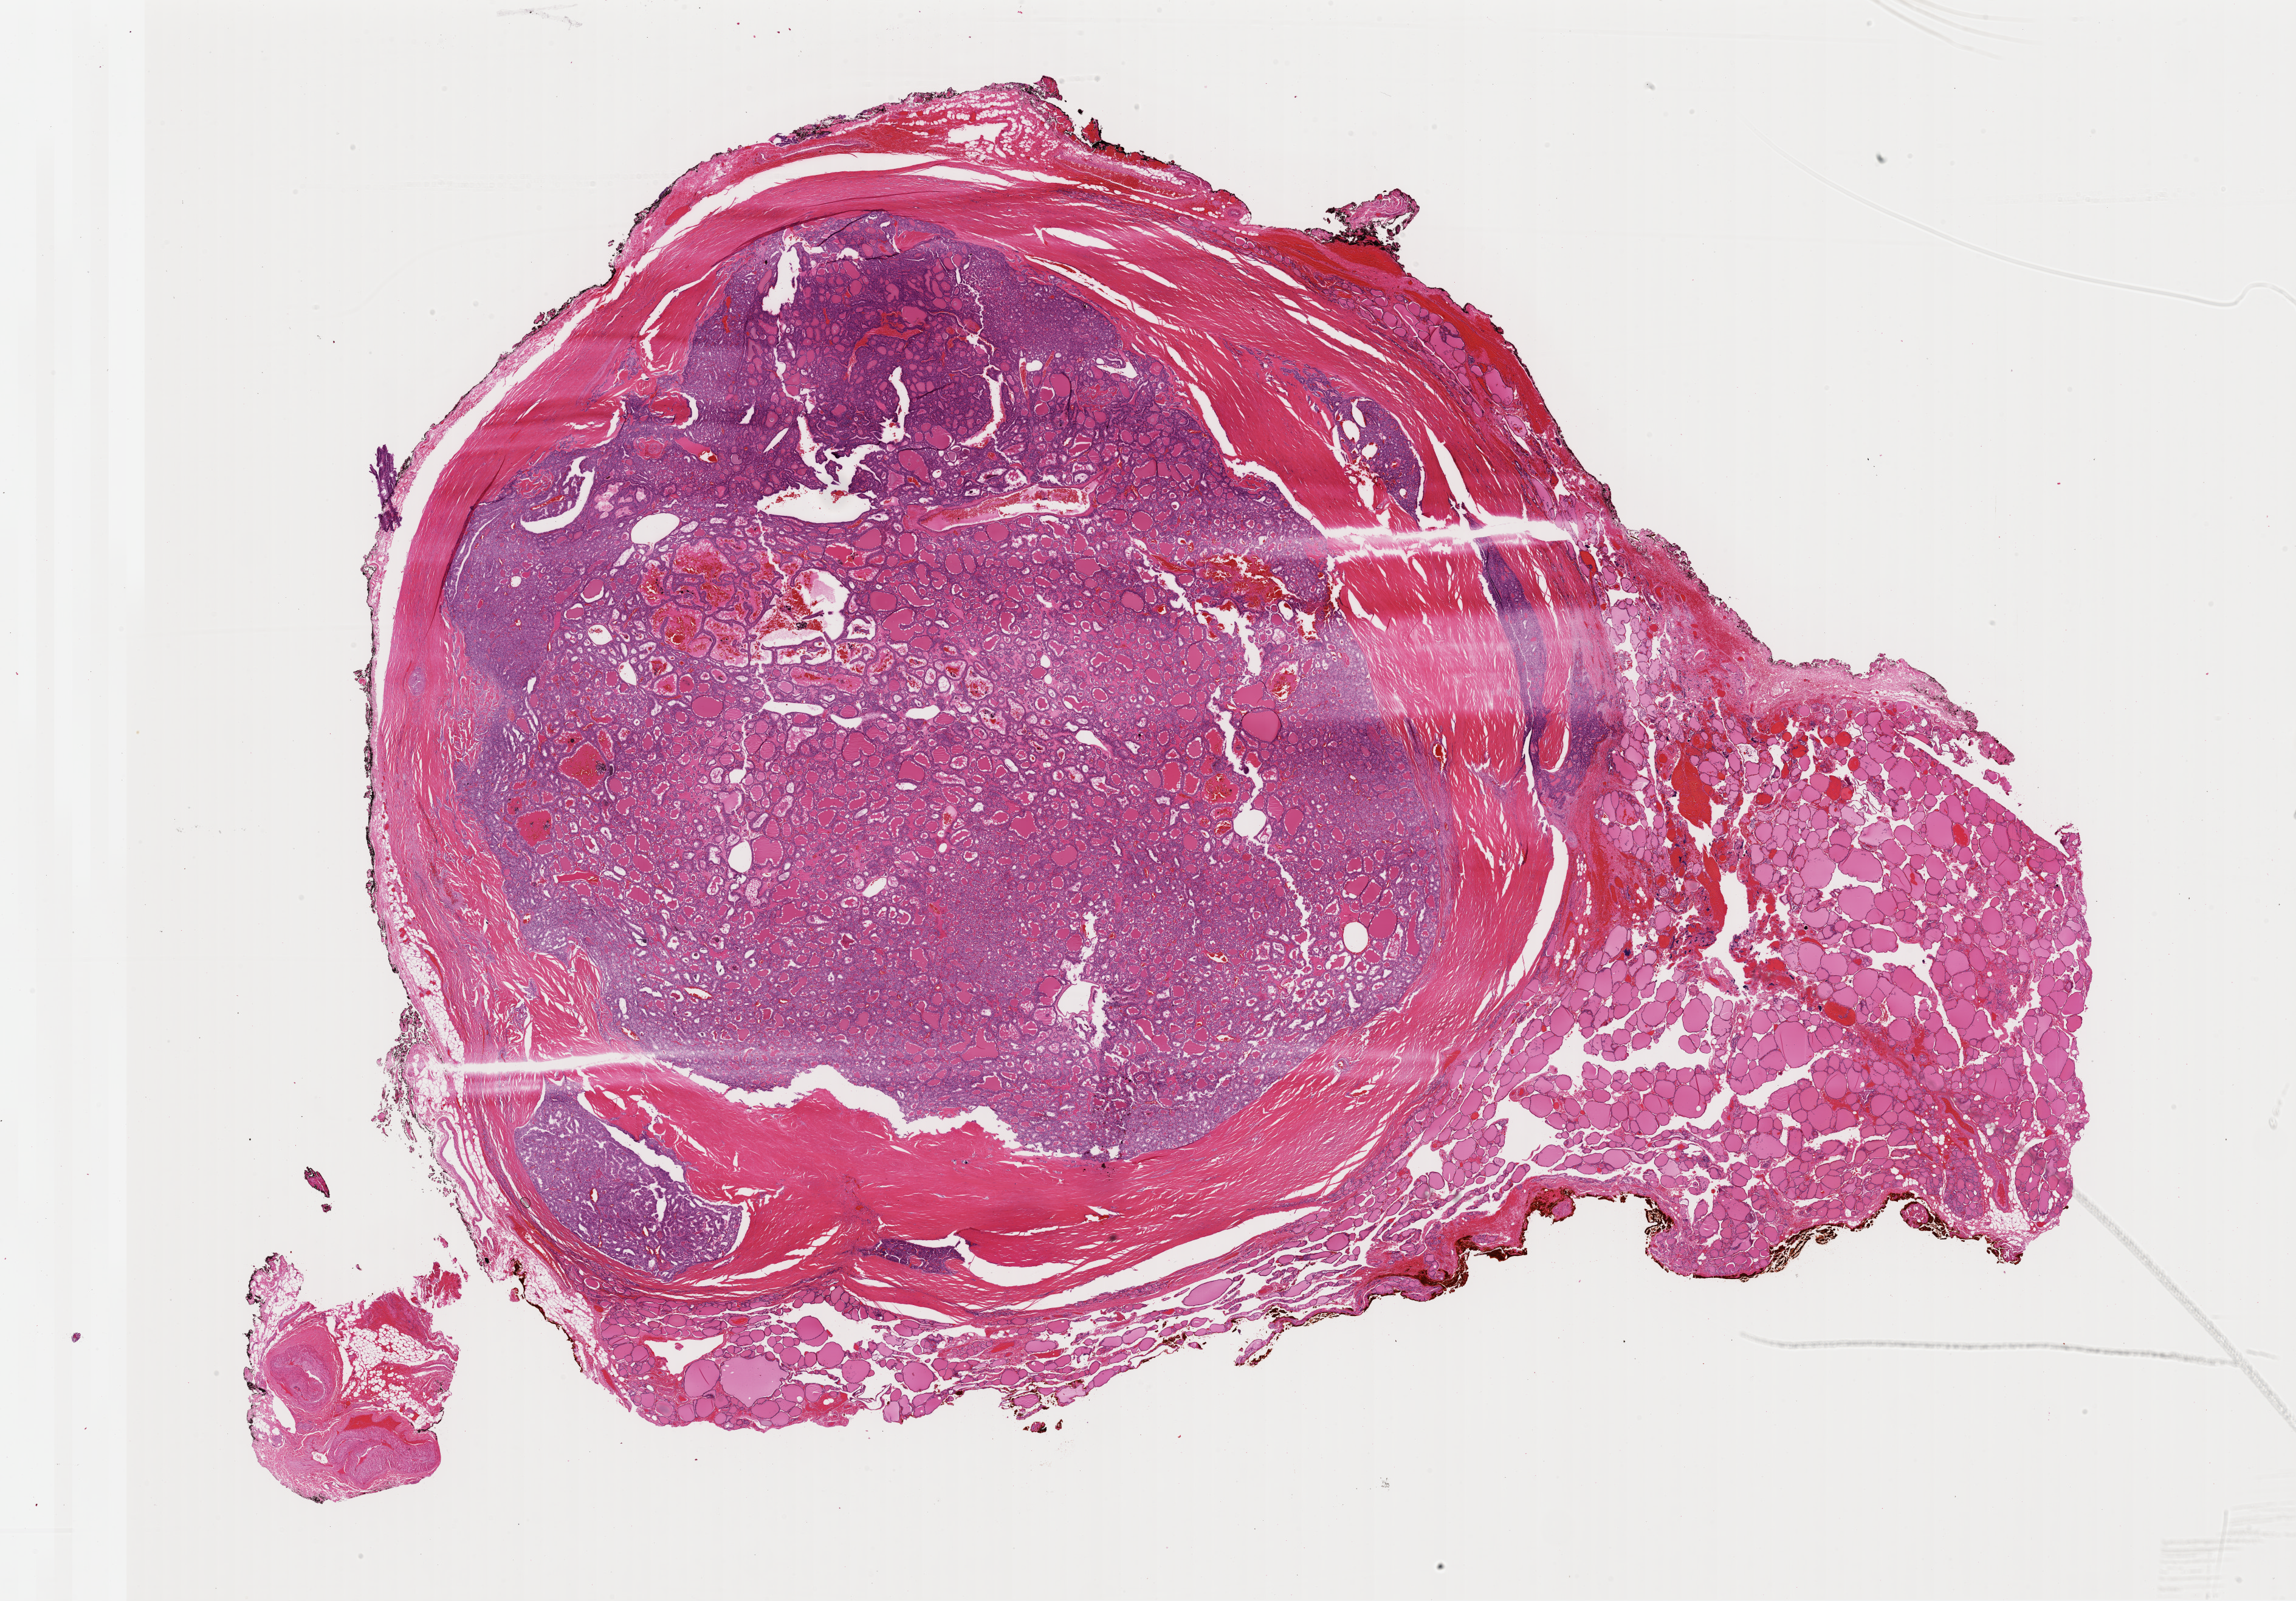
Digitized Hematoxylin and eosin (H&E) stained tissue section (whole slide) — whole scanned area (about 29.8 x 20.8 mm, slide scanned at 40x) shown as a low-resolution overview, formalin-fixed paraffin-embedded (FFPE) diagnostic section, primary tumour sample from the thyroid. Female, age 34 years at initial diagnosis.
AJCC pathologic stage: I (6th edition). Diagnosis: Papillary adenocarcinoma, NOS (thyroid gland). Lymph nodes positive (case pathology): 2 of 3 examined. Laterality: left.